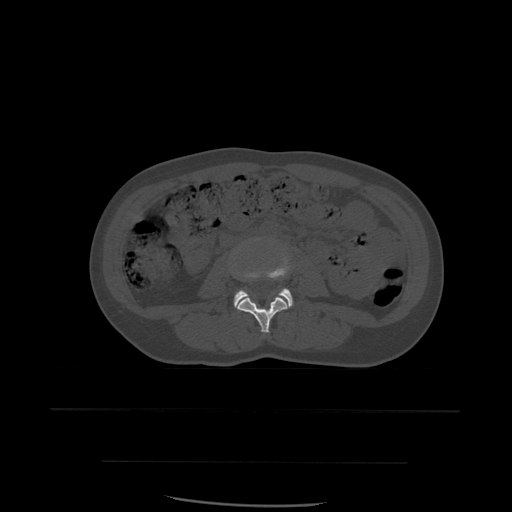
CT including the spine, one axial slice; slice 186 of 574 in the series (ordered by position); bone window (W 1800 / L 400 HU); 1.25 mm slice thickness; 512 × 512 image matrix. Patient age 48 years. Case-level facts recorded for this patient, not image findings: primary cancer: lung.
Outlined on this slice (semi-automatically segmented with operator editing):
- L3 vertebra: bounding box [x1, y1, x2, y2] px = [235, 297, 288, 334]
- L4 vertebra: [234, 257, 293, 308]